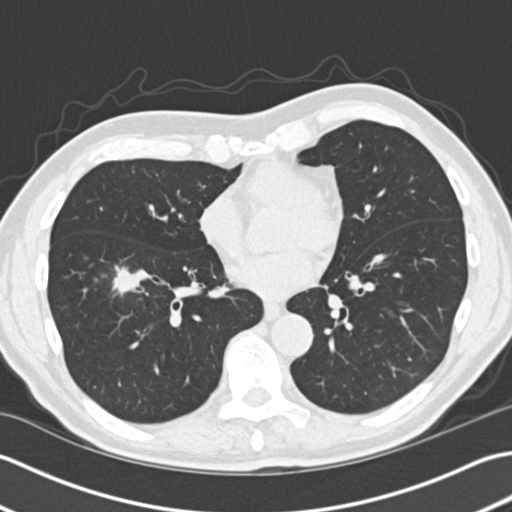
Low-dose screening chest CT, one axial slice. Slice 70 of 172 in the series (ordered by position). Reconstruction kernel B30f. Lung window (W 1500 / L -600 HU). 512 × 512 image matrix, field of view 350 × 350 mm.
Structures marked on this image (outlined manually by an expert reader):
- lesion 1 (tumor, lower lobe of right lung): bounding box [x1, y1, x2, y2] px = [112, 265, 153, 296]